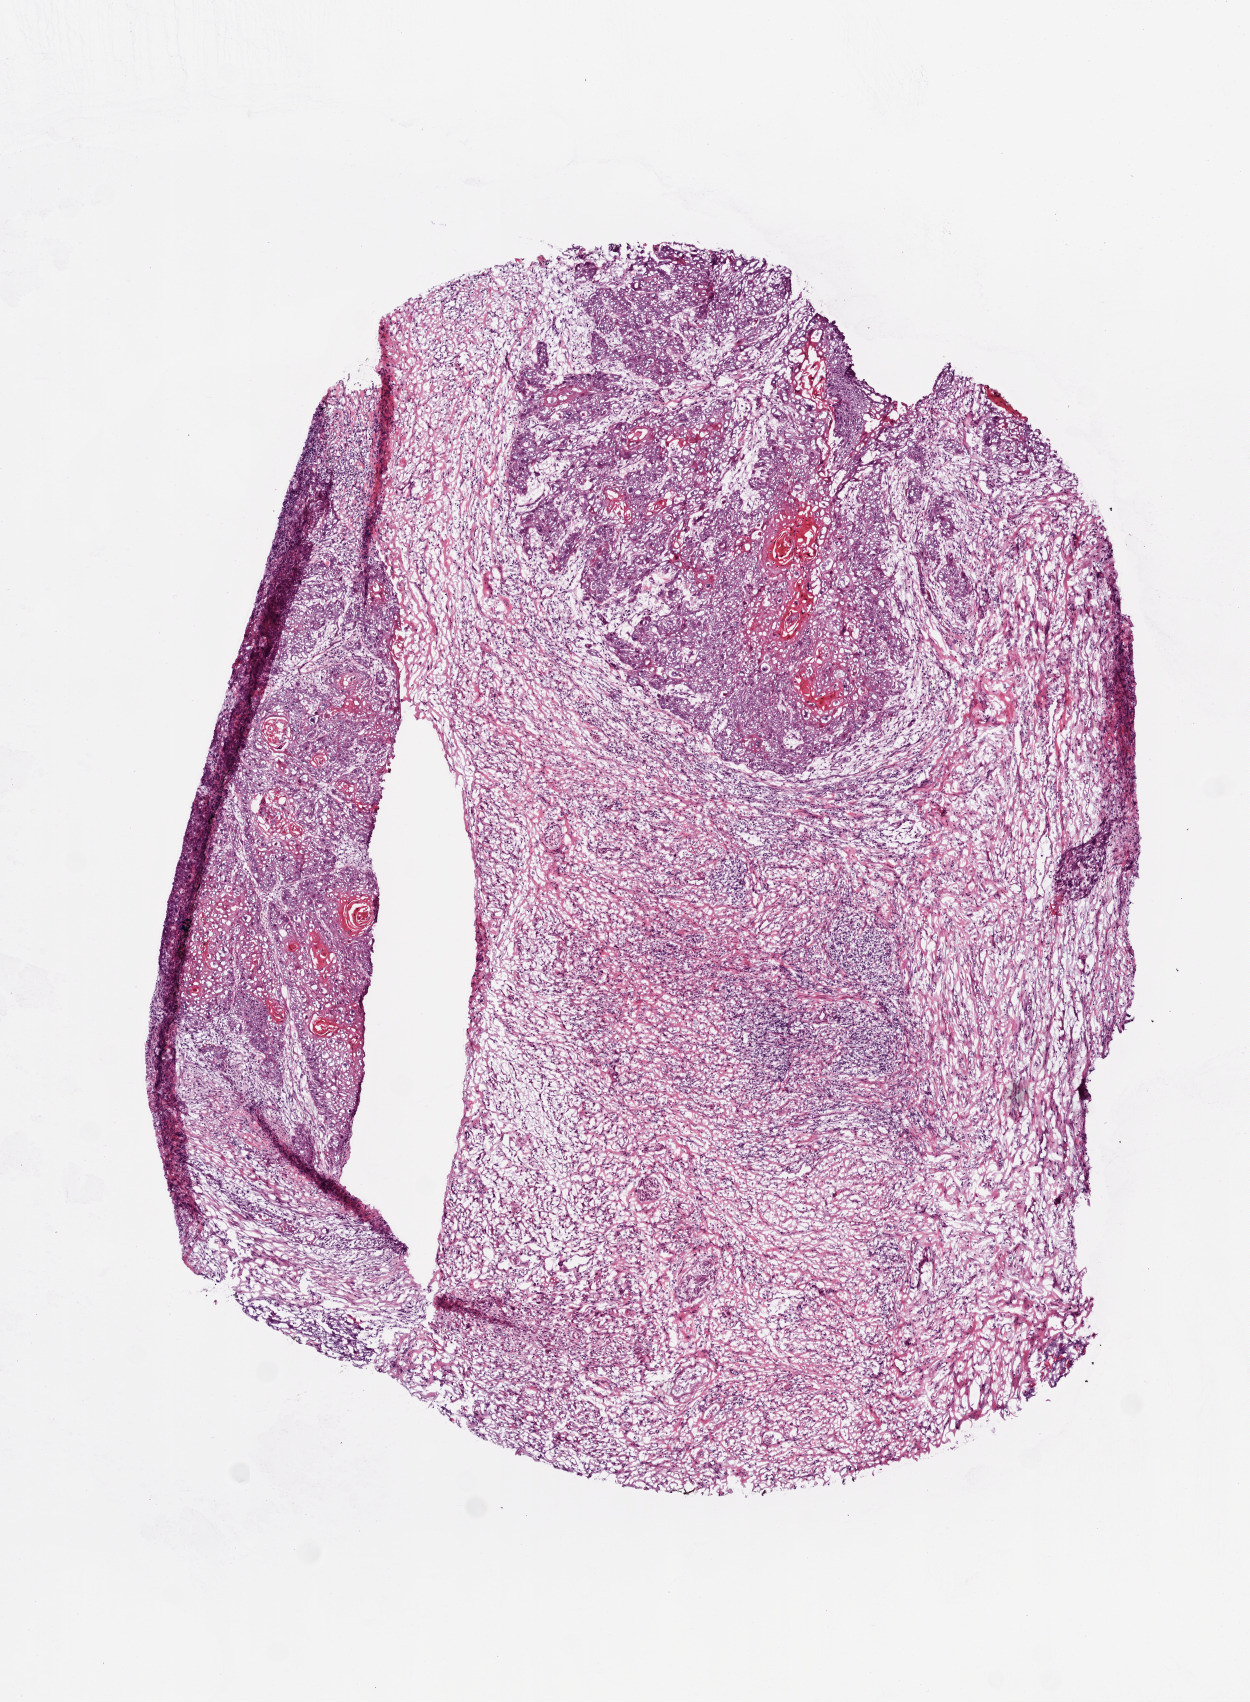
Whole-slide histology image, Hematoxylin and eosin (H&E) stained — a low-resolution overview of the entire scanned area, about 5.0 x 6.8 mm; frozen section from the top of the tissue portion; head and neck, primary tumour sample. Male patient; age at initial diagnosis 64 years.
Diagnosis: Squamous cell carcinoma, NOS (larynx, NOS).